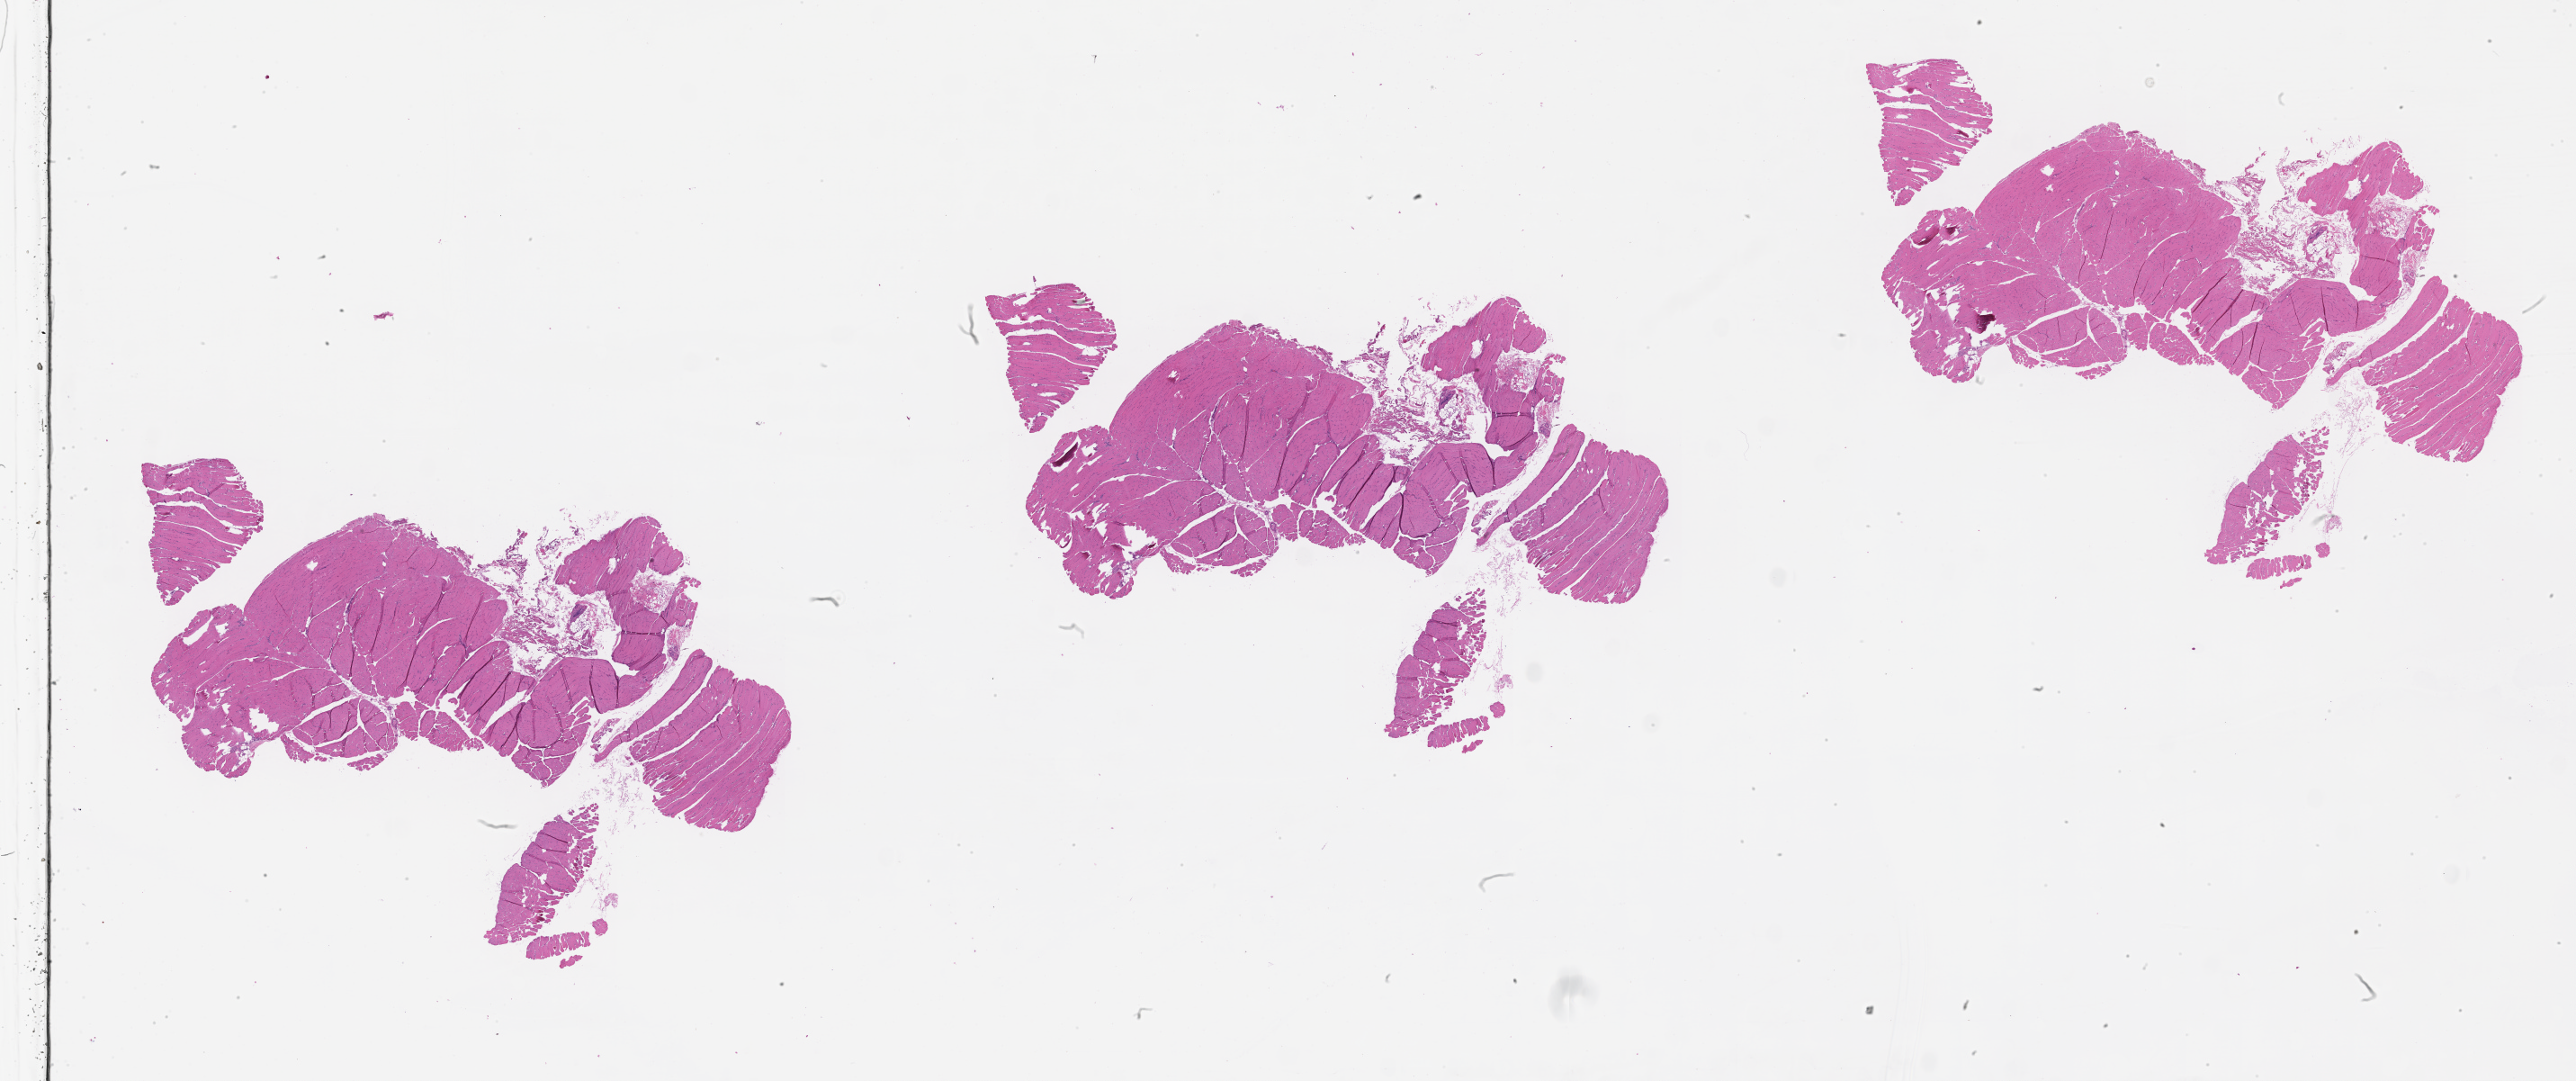
H&E whole-slide image — a low-resolution overview of the entire scanned area, about 46.1 x 19.3 mm (slide scanned at 20x).
Patient diagnosis (cohort enrolment): sarcoma (site not recorded at cohort level).